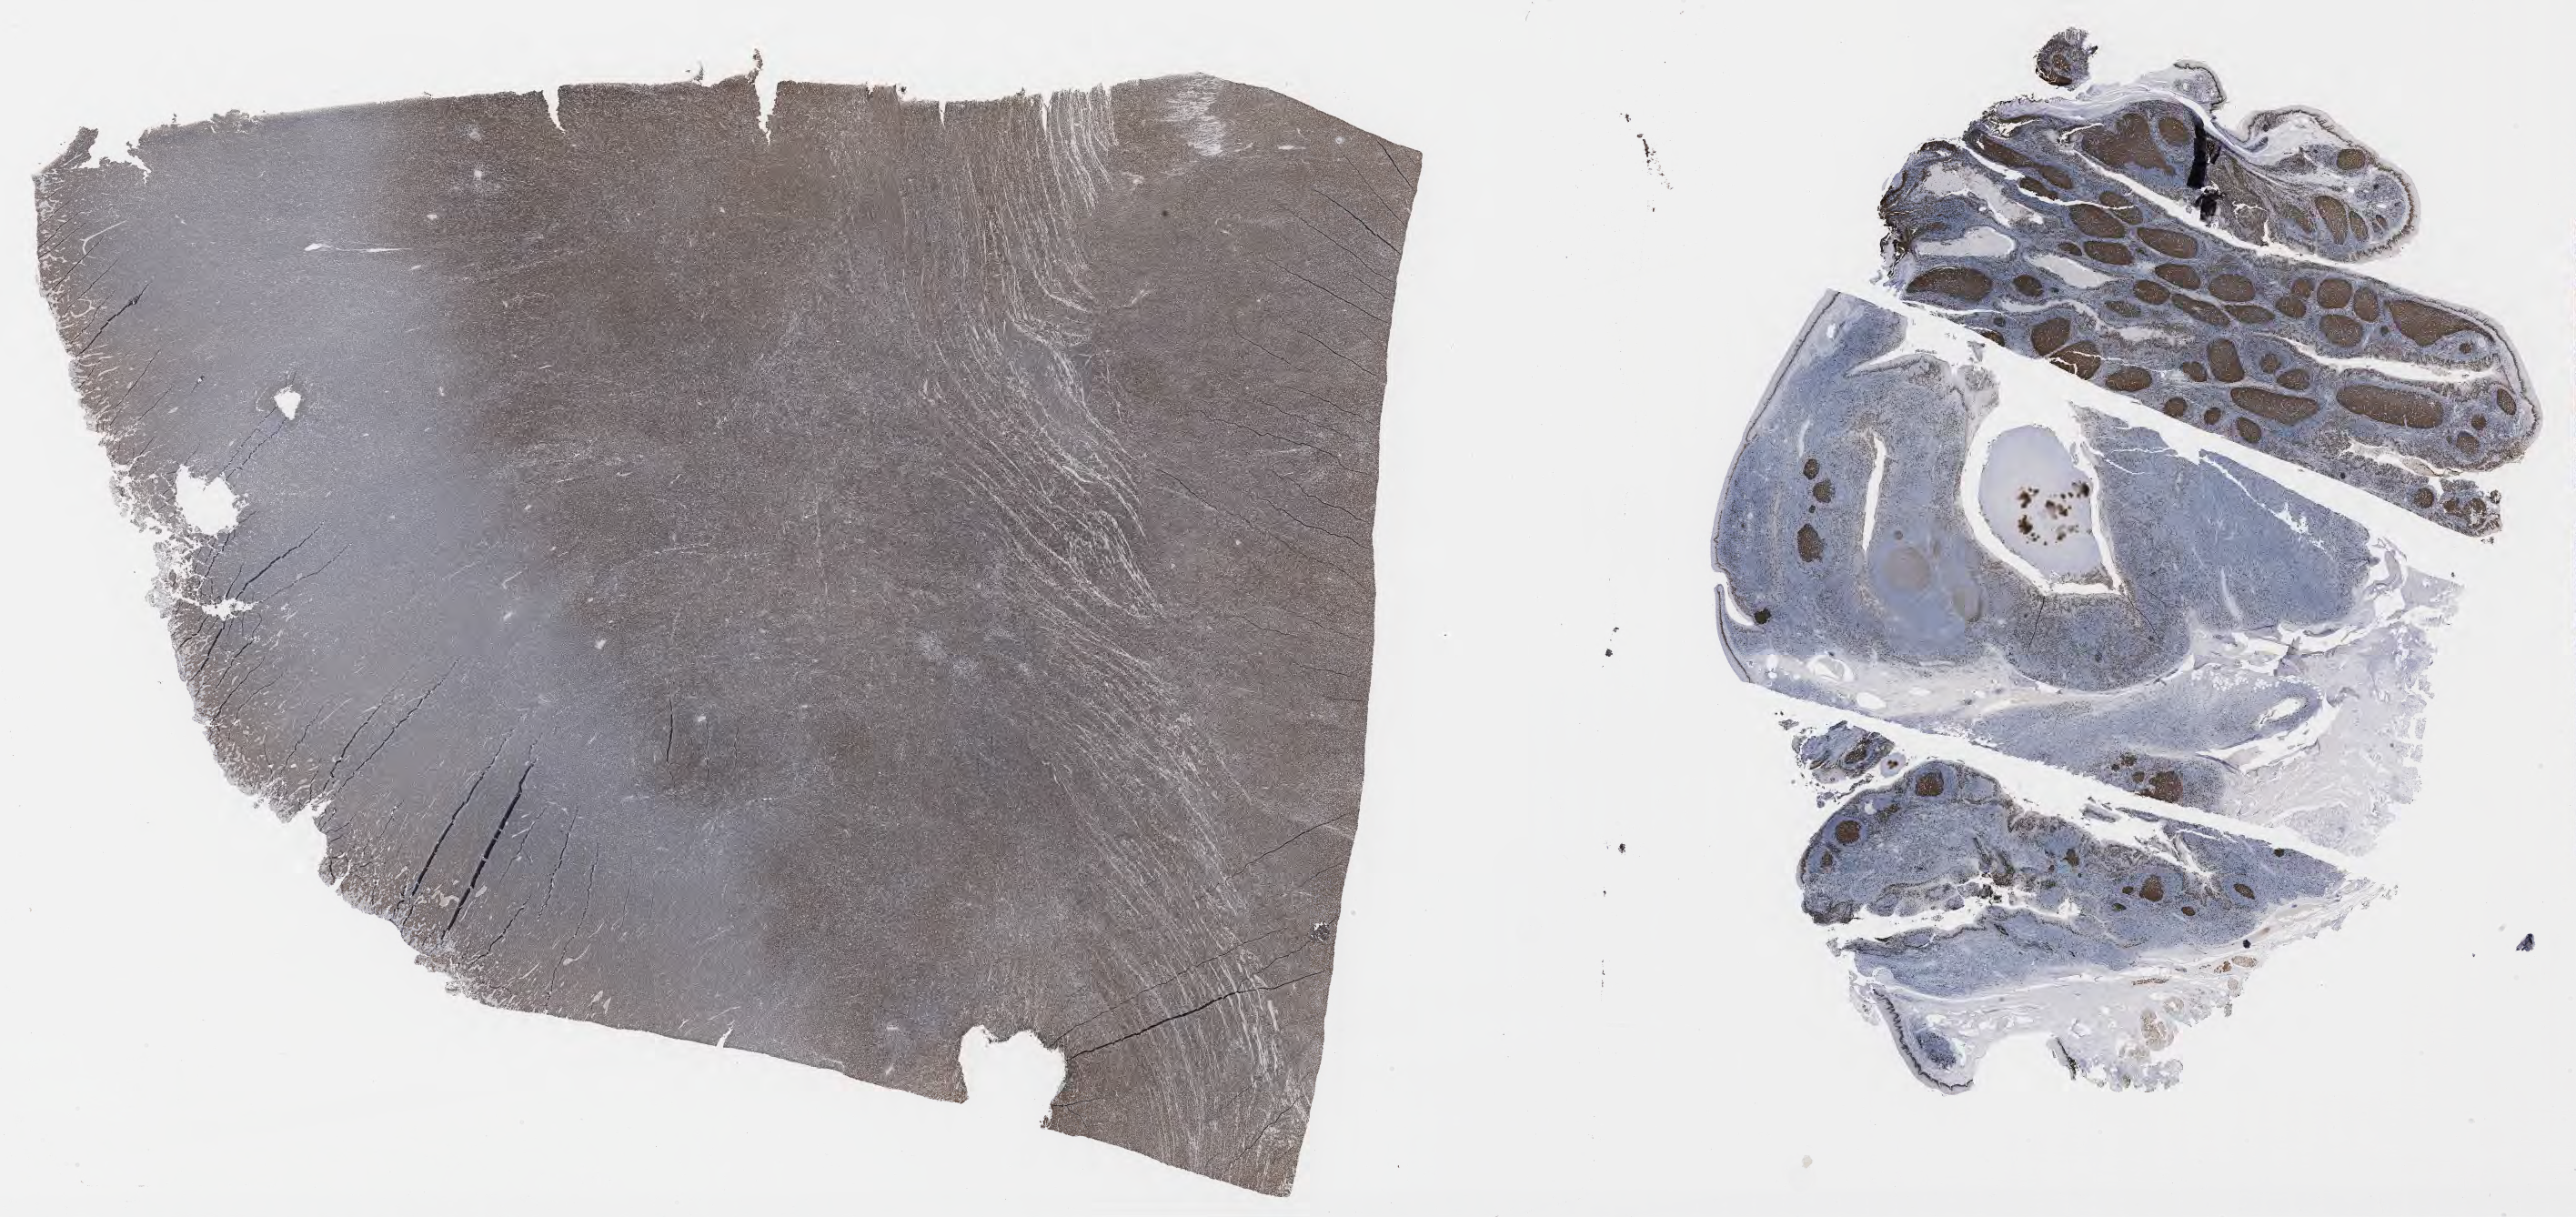
IHC for Ki-67, whole-slide image — shown as a low-resolution overview of the whole scanned area (about 45.8 x 21.6 mm). Specimen: tumor tissue. Patient: male, aged 17.
Diagnosis: Burkitt lymphoma, NOS.